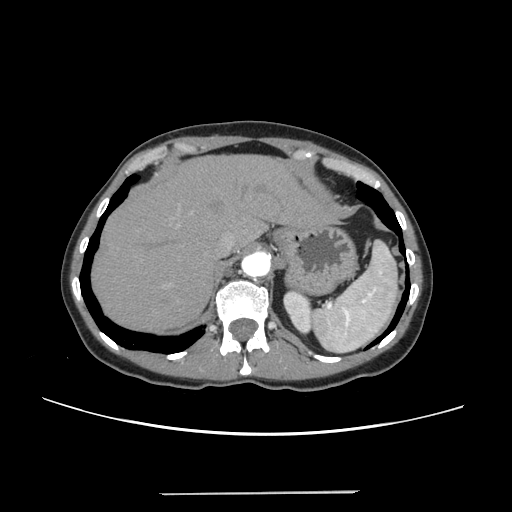
Contrast-enhanced abdominal CT, one axial slice; intravenous contrast given; soft-tissue window (W 400 / L 40 HU); 1.25 mm slice thickness; 512 × 512 image matrix, field of view 371 × 371 mm. Female patient, age 60 years. From the clinical record (not read from this slice): diagnosis: colorectal cancer liver metastases, imaged before liver resection; multiple liver metastases: no; largest metastasis: 1.5 cm; chemotherapy before resection: yes.
Structures marked on this image (expert manual segmentation):
- hepatic veins: bounding box [x1, y1, x2, y2] px = [221, 234, 234, 251]
- liver: [93, 156, 327, 331]
- planned liver remnant (the part of the liver to remain after resection): [93, 156, 328, 331]